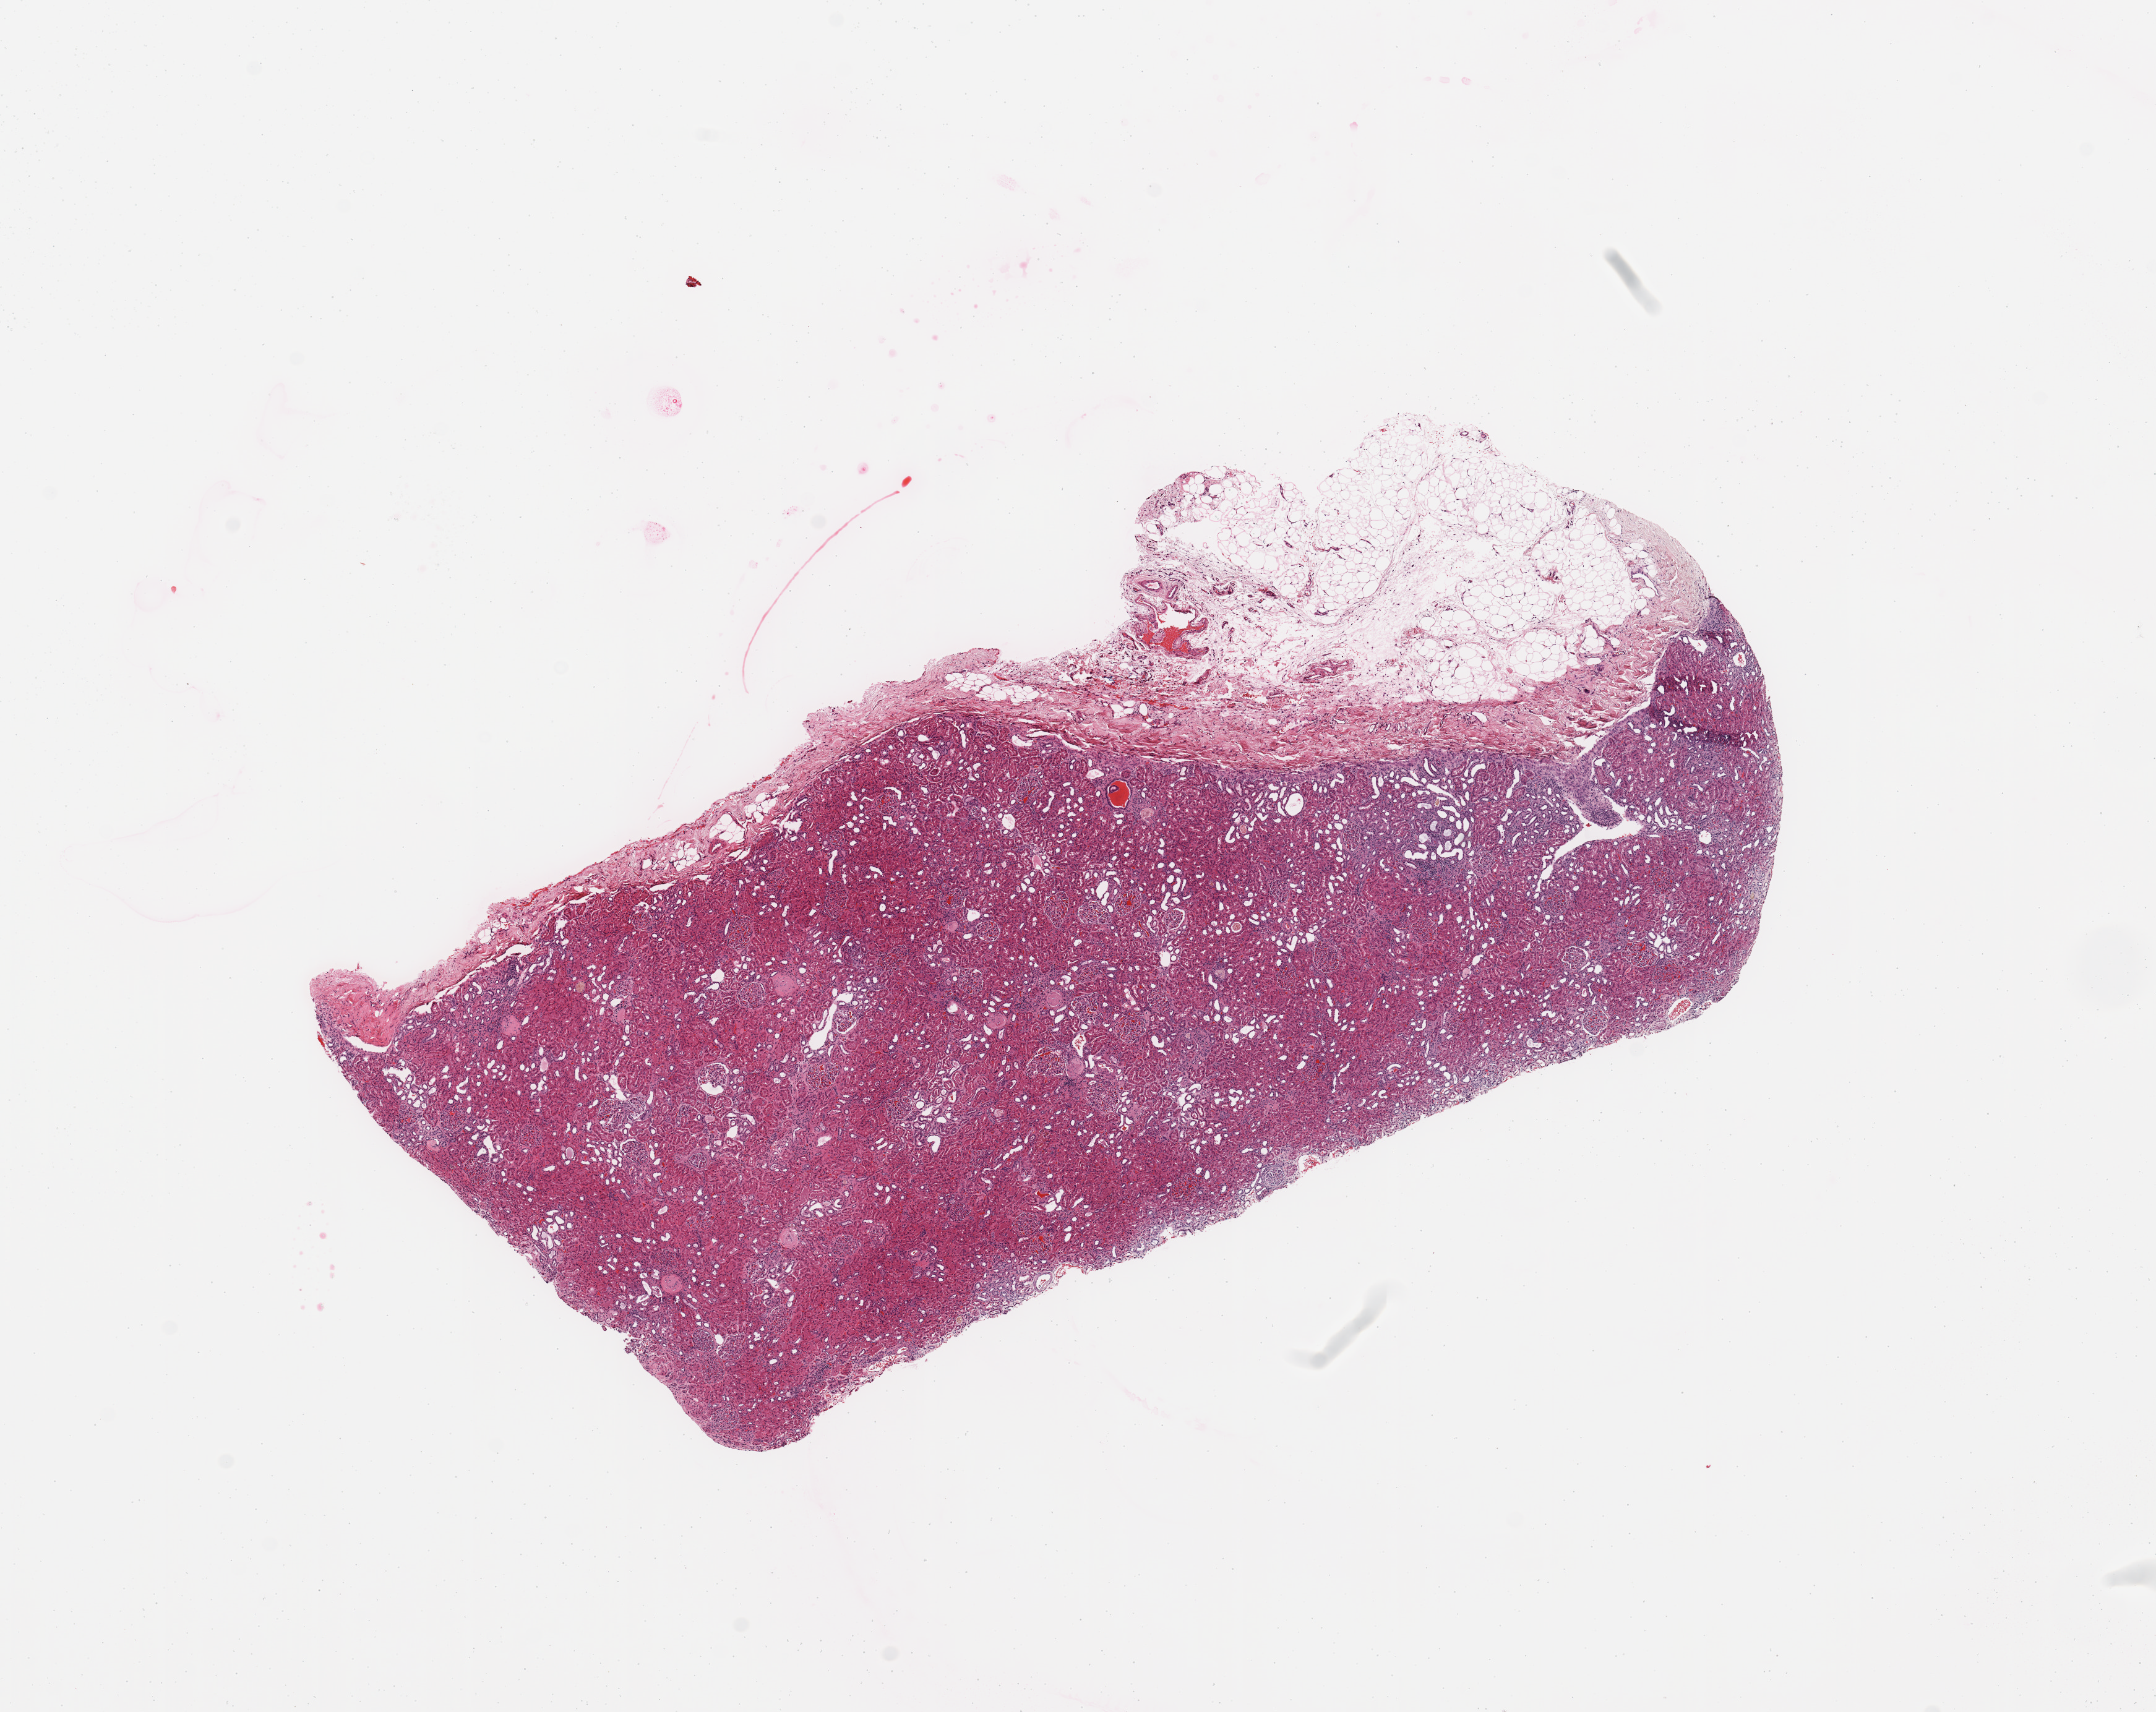
Whole-slide histology image, Hematoxylin and eosin (H&E) stained — low-resolution overview of the scanned area, about 13.8 x 10.9 mm (acquisition: 20x scan). Normal (non-tumour) tissue sample, sampled site: kidney. Patient: female, age 54 years.
* this section: normal (non-tumour) tissue from the same patient
* patient diagnosis: Renal cell carcinoma, NOS